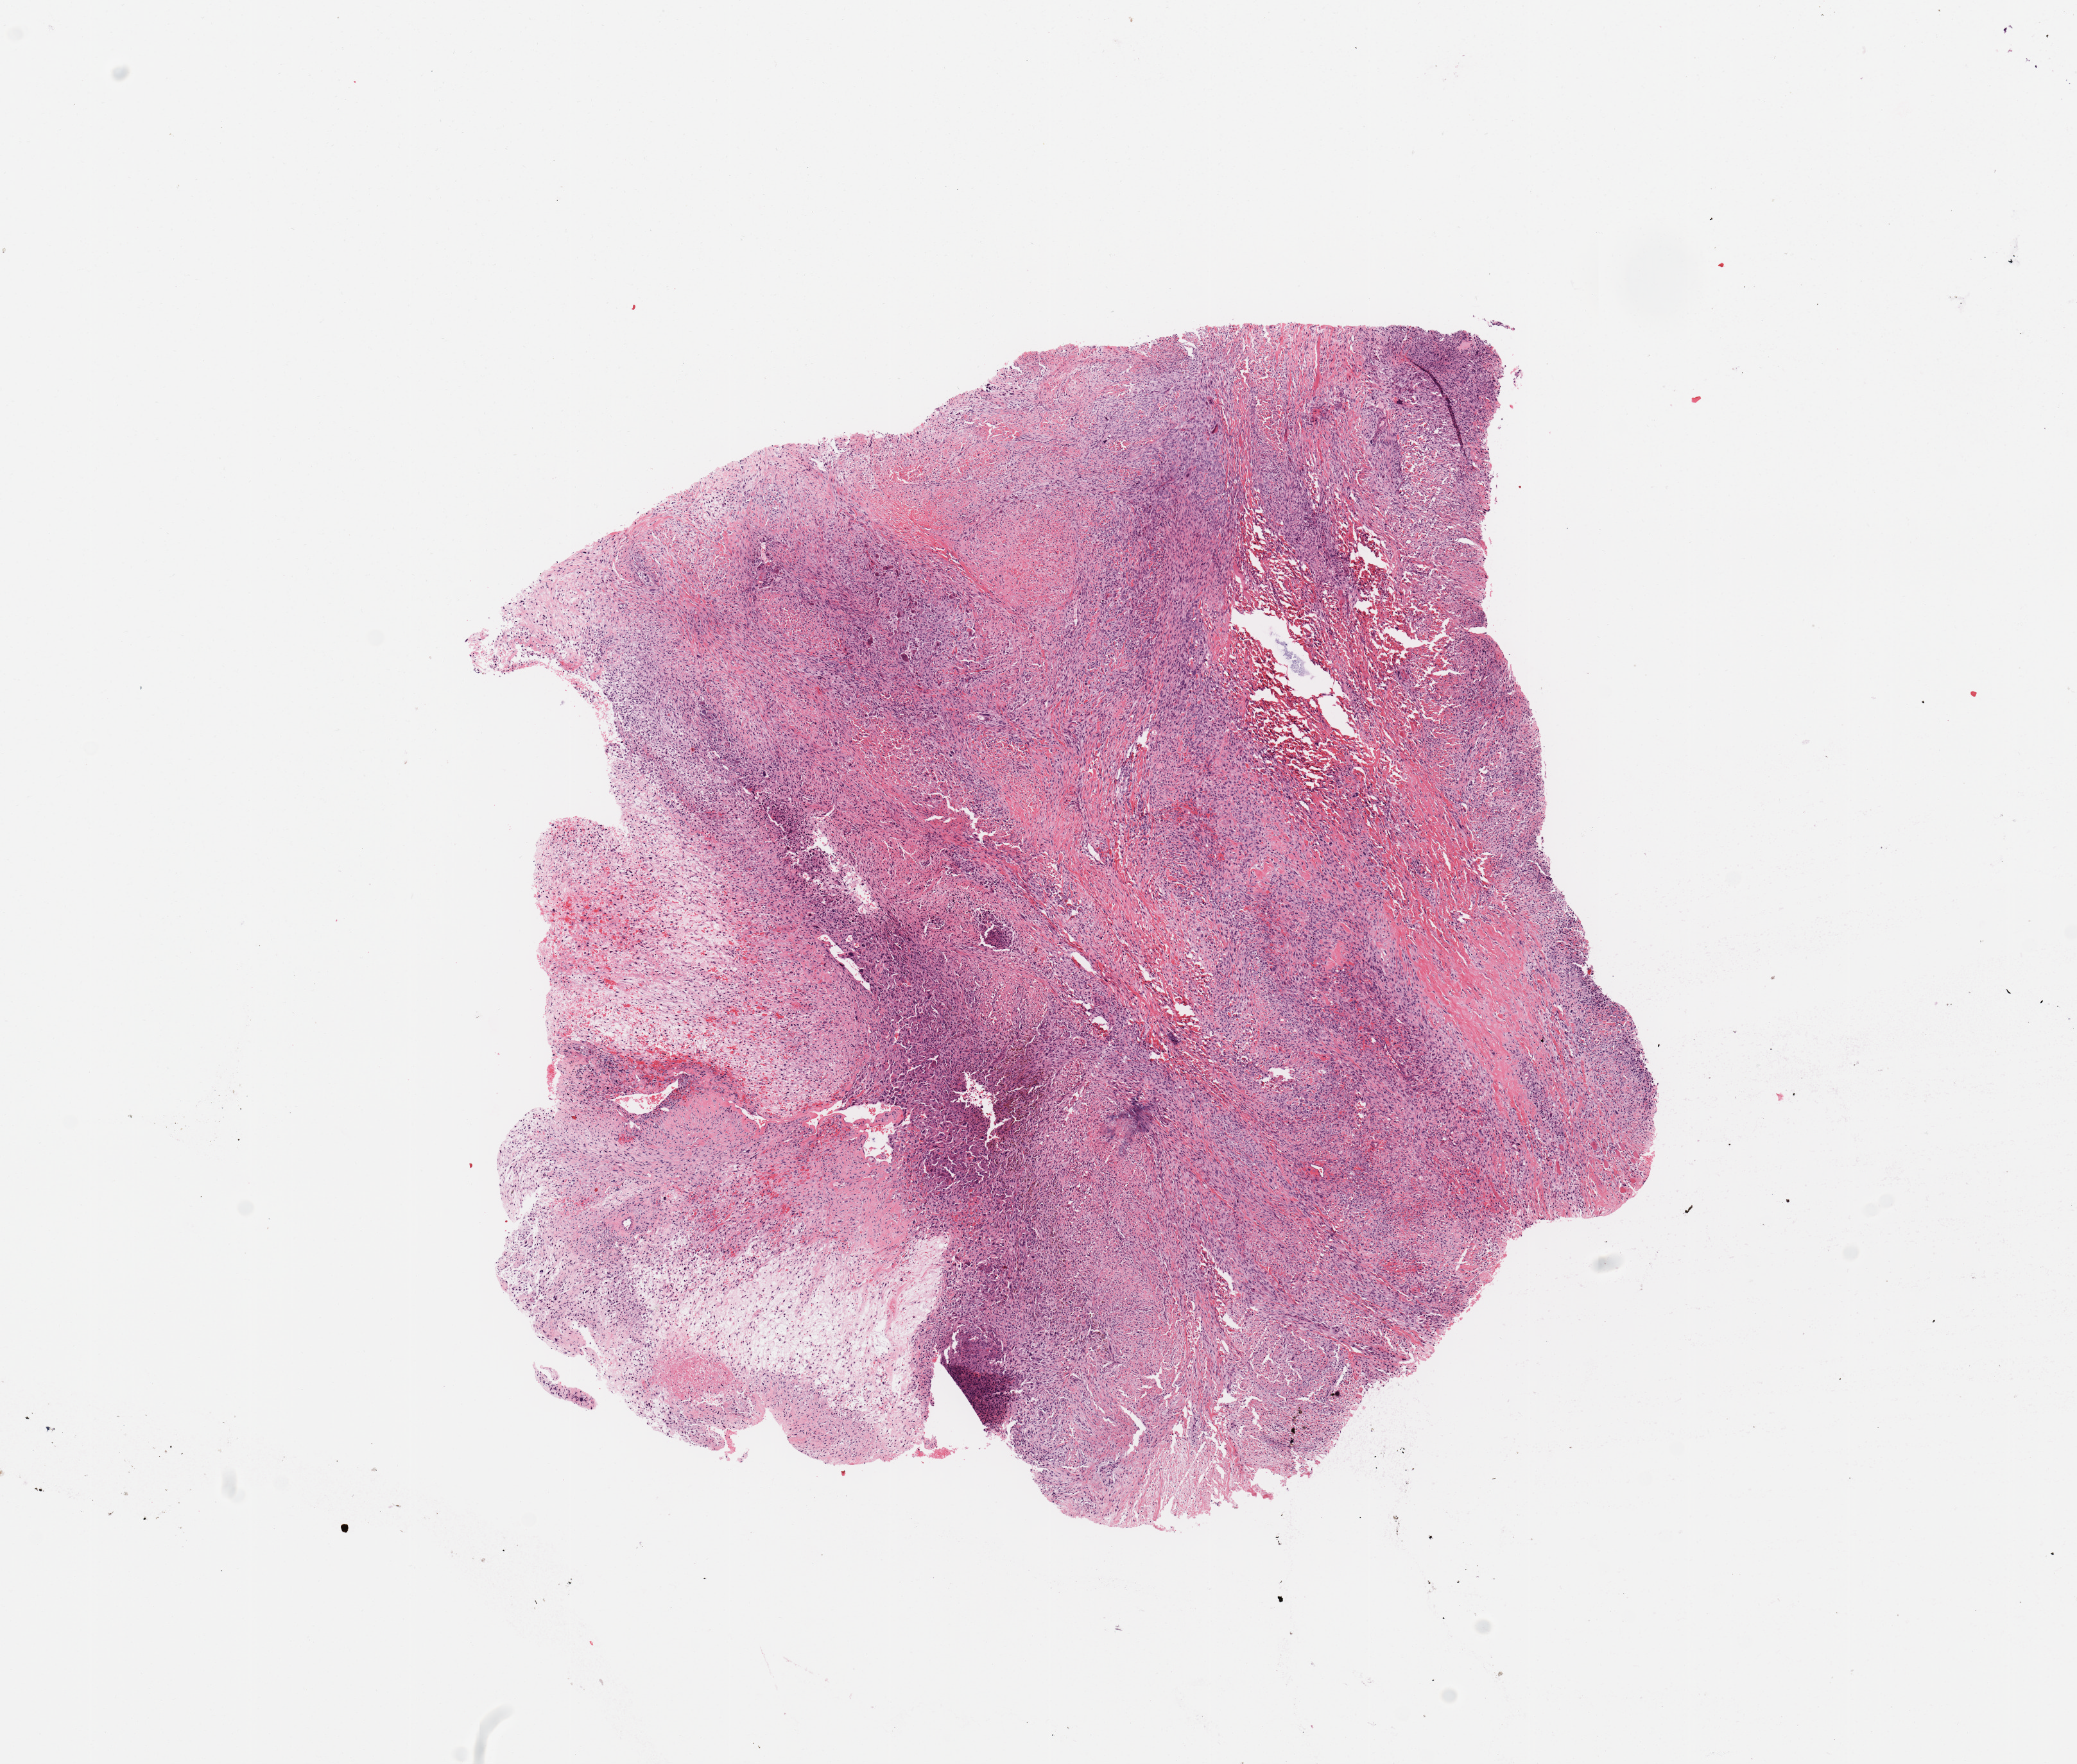
Hematoxylin and eosin (H&E) stained whole-slide image, a low-resolution overview of the entire scanned area, about 12.8 x 10.9 mm (acquisition: 20x scan). Tumour tissue sample. Male, 54 y/o.
Patient diagnosis (cohort enrolment): sarcoma (site not recorded at cohort level). Primary tumour site (as recorded): upper extremity.